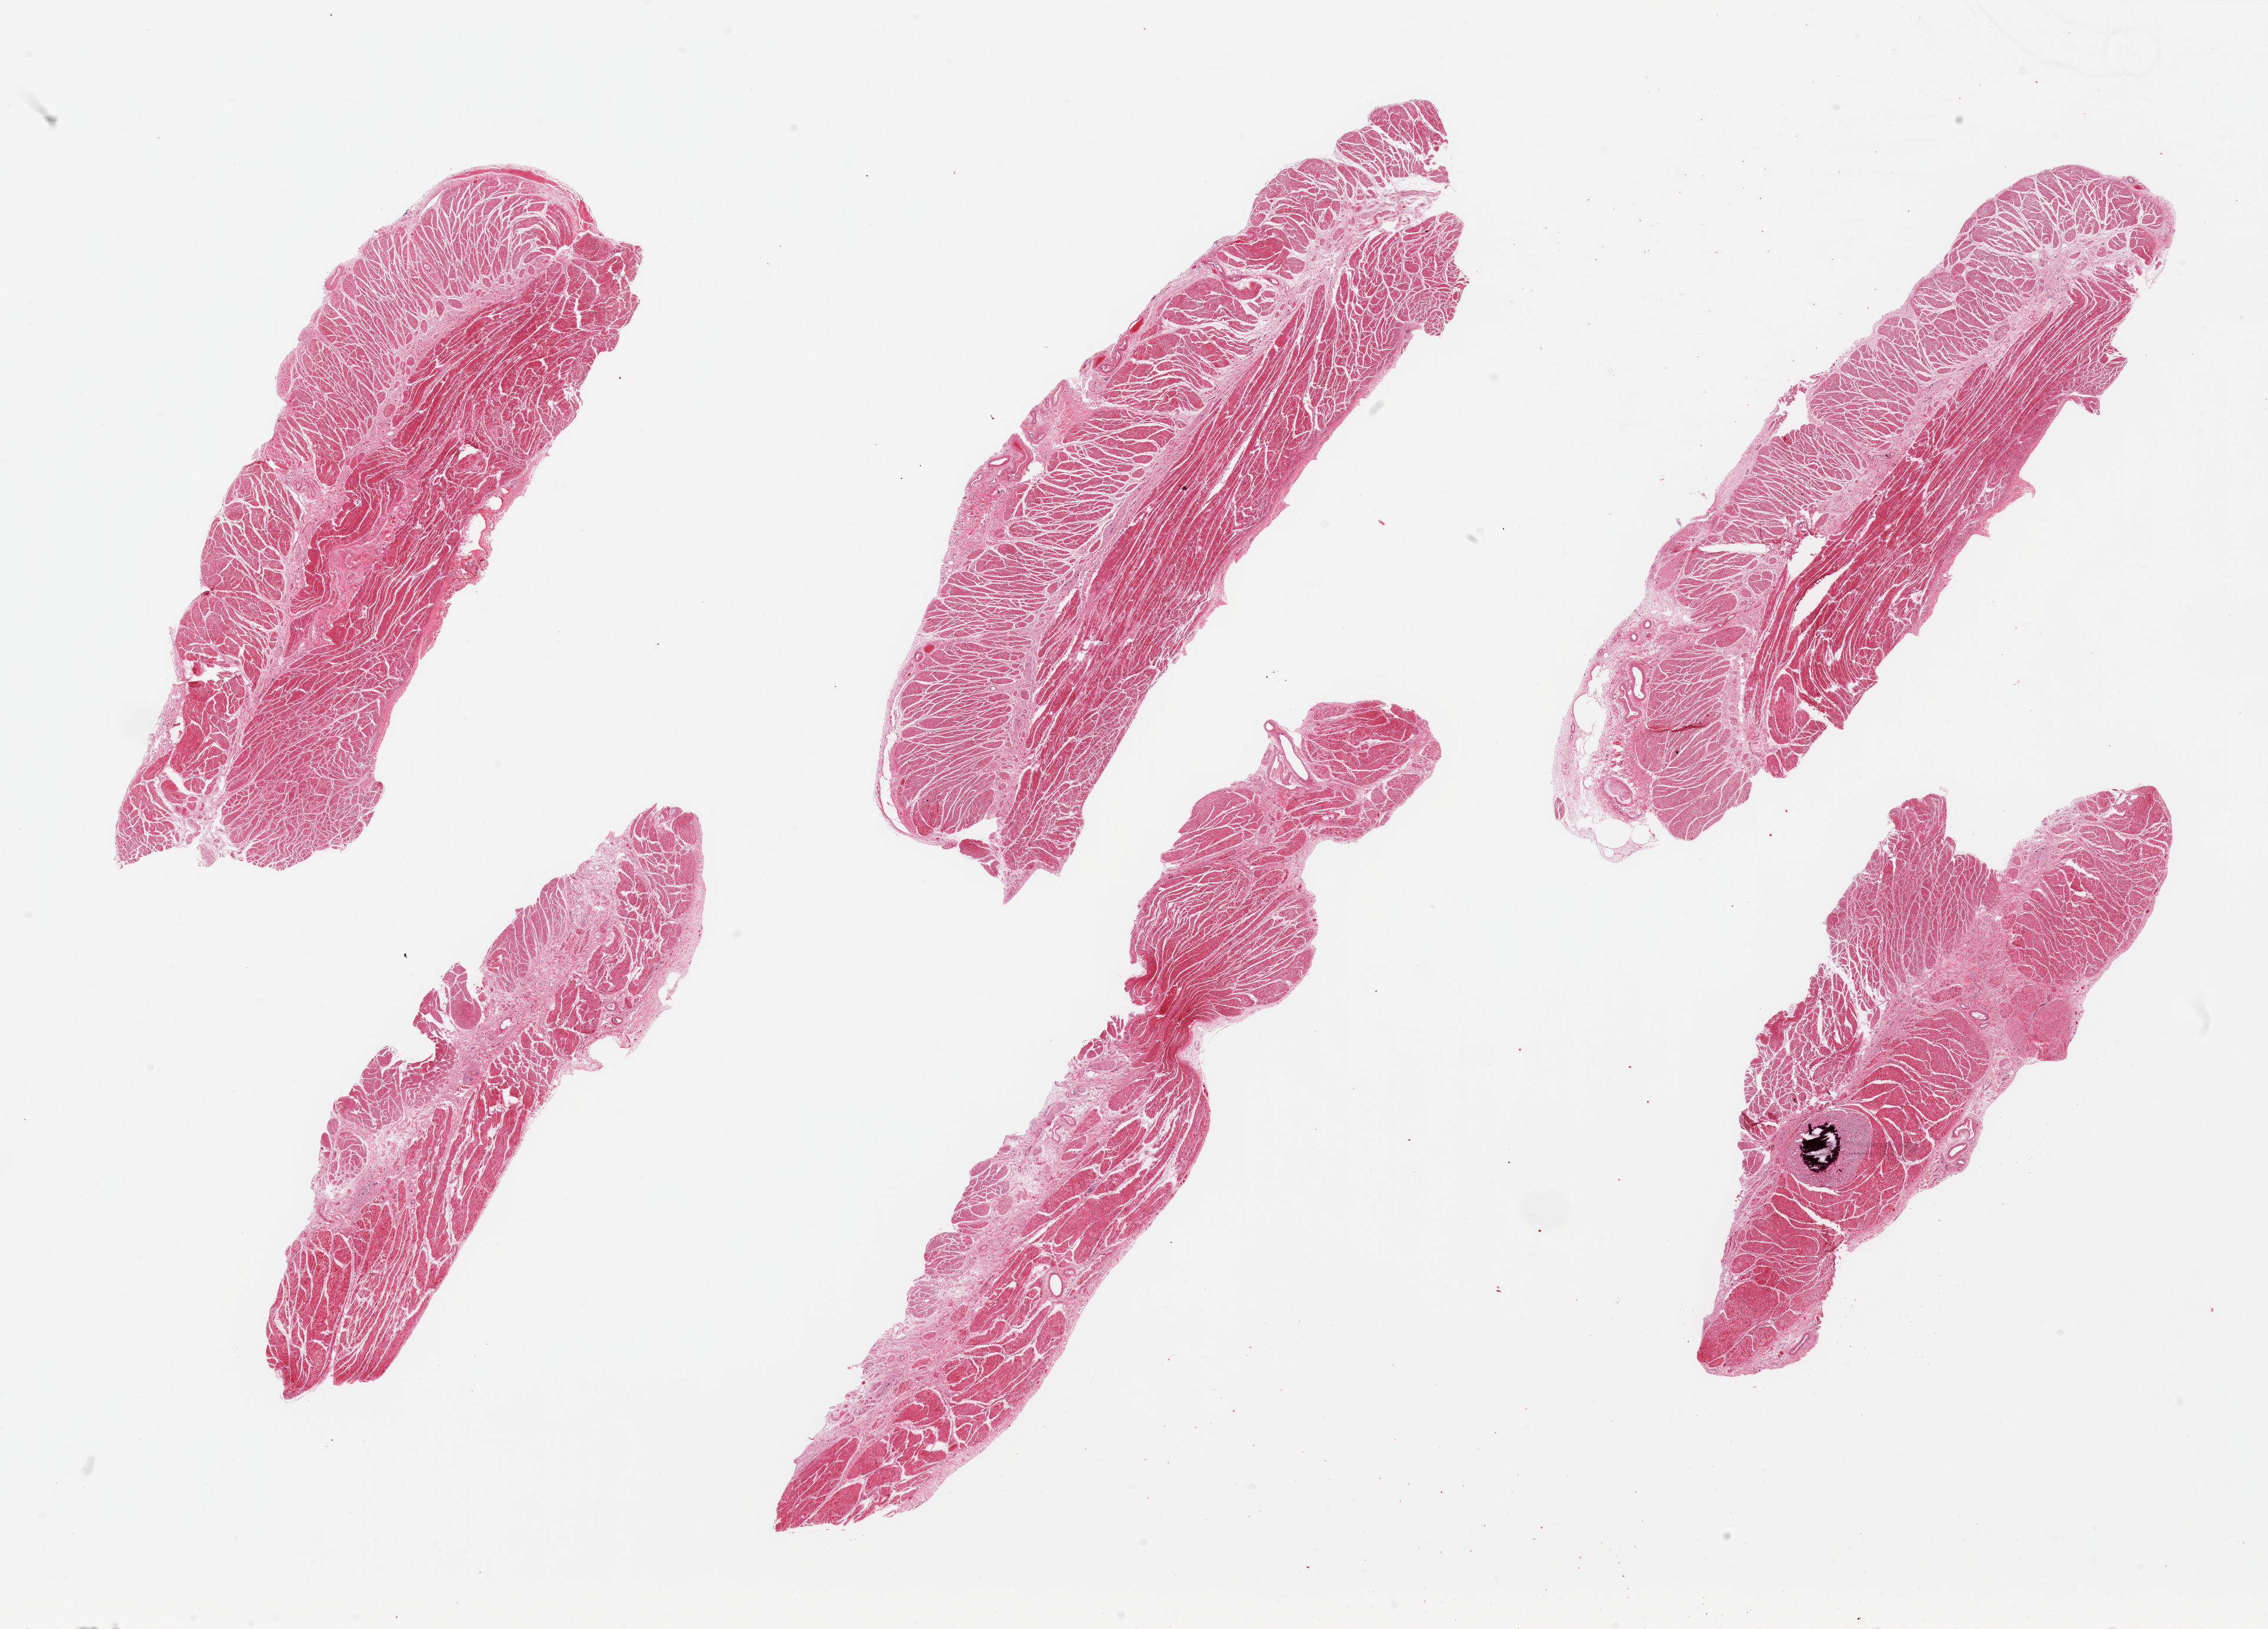
Digitized hematoxylin and eosin (H&E)-stained section — whole scanned area (about 30.5 x 21.9 mm, acquisition: 20x scan) shown as a low-resolution overview, PAXgene-fixed paraffin-embedded (PFPE) section, sampled site (target tissue): gastroesophageal junction, donor tissue sample. Female donor.
Pathologist's review note for this sample: 6 pieces; 1 mm partly calcified leiomyoma in 1 of 6 pieces.